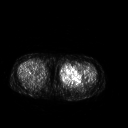
FDG PET of an extremity soft-tissue mass (from a PET/CT study), one axial slice. 128 × 128 image matrix, field of view 500 × 500 mm. Female patient, age 42 years. From the clinical record (not read from this slice): histological type: pleiomorphic leiomyosarcoma; grade: intermediate; site of the primary tumour: left thigh.
Outlined on this slice (expert contour drawn on MRI and transferred to this co-registered scan by the dataset authors):
- gross tumour volume including surrounding oedema: box from (x=59, y=65) to (x=83, y=84) px
- gross tumour volume (mass): (x=59, y=65)–(x=82, y=84)